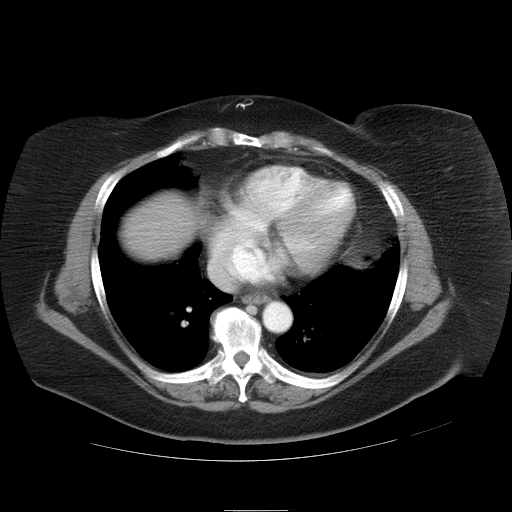
Contrast-enhanced abdominal CT, one axial slice. Slice 35 of 37 in the series (ordered by position). Soft-tissue window (W 400 / L 40 HU). 512 × 512 image matrix, field of view 422 × 422 mm. Female patient, age 68 years. From the clinical record (not read from this slice): diagnosis: colorectal cancer liver metastases, imaged before liver resection; multiple liver metastases: no; largest metastasis: 2 cm; chemotherapy before resection: no.
Structures marked on this image (manually delineated by an expert):
- liver: box from (x=120, y=193) to (x=199, y=259) px
- planned liver remnant (the part of the liver to remain after resection): (x=120, y=193)–(x=199, y=259)